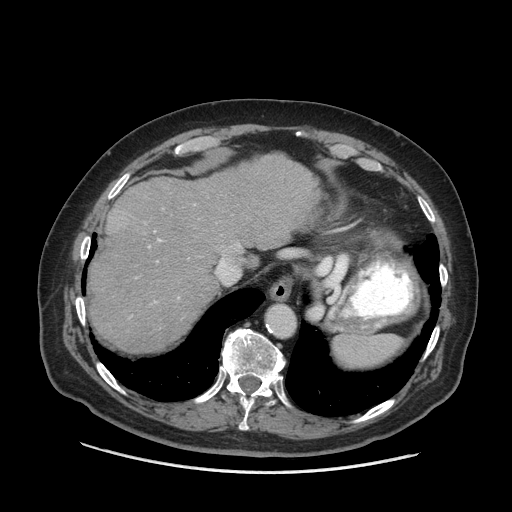
Contrast-enhanced abdominal CT (liver protocol), one axial slice. Reconstruction kernel STANDARD. 140 kVp. Soft-tissue window (W 400 / L 40 HU). 2.5 mm slice thickness. 512 × 512 image matrix, field of view 420 × 420 mm. Case-level facts recorded for this patient, not image findings: diagnosis: hepatocellular carcinoma (patient treated with transarterial chemoembolisation; whether this scan precedes or follows treatment is not stated here); TNM stage (as recorded): Stage-I.
Annotated regions visible in this slice (semi-automatically segmented with operator editing):
- abdominal aorta: bounding box [x1, y1, x2, y2] px = [267, 306, 295, 335]
- liver parenchyma outside the tumour (the mass and vessels are separate outlines, so this box may not span the whole liver): [88, 154, 320, 352]
- mass: [107, 207, 130, 233]
- liver vessels: [149, 239, 162, 247]